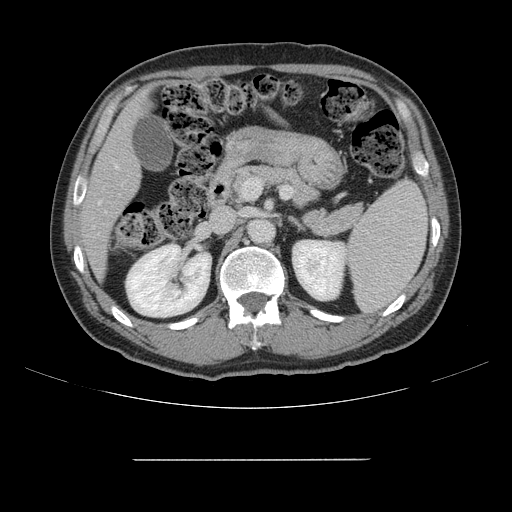
Contrast-enhanced abdominal CT, one axial slice; intravenous contrast given; soft-tissue window (W 400 / L 40 HU); 512 × 512 image matrix, field of view 404 × 404 mm. Male patient, age 54 years. Case-level facts recorded for this patient, not image findings: diagnosis: colorectal cancer liver metastases, imaged before liver resection; multiple liver metastases: yes.
Annotated regions visible in this slice (outlined manually by an expert reader):
- hepatic veins: bounding box <98,165,118,204> (left, top, right, bottom; pixels)
- liver: <85,98,144,276>
- planned liver remnant (the part of the liver to remain after resection): <85,96,146,276>